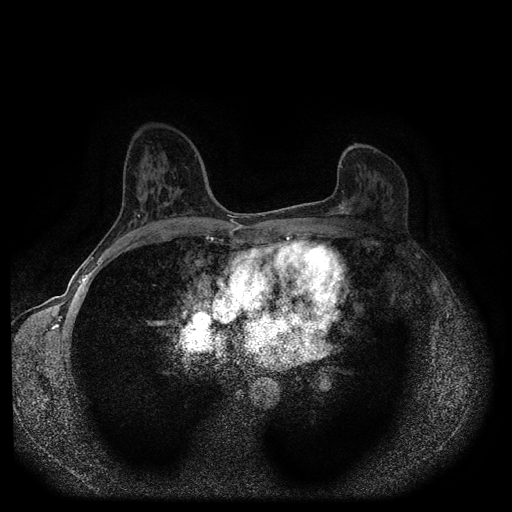
Breast MRI (dynamic contrast-enhanced, multi-phase), one axial slice. Position 56 of 116 along the scan axis. Dynamic contrast-enhanced series, time point 2 of 5 at this slice position (early post-contrast). 1.5 T. TE 2.6 ms, TR 5.4 ms. 2 mm slice thickness. 512 × 512 image matrix, field of view 340 × 340 mm. Patient: female, 57 years.
Annotated regions visible in this slice (semi-automatic segmentation, software-assisted and operator-edited):
- breast lesion (labelled 'tumour' in the annotation; benign lesions carry a separate 'benign' label): bounding box <338,198,349,217> (left, top, right, bottom; pixels)